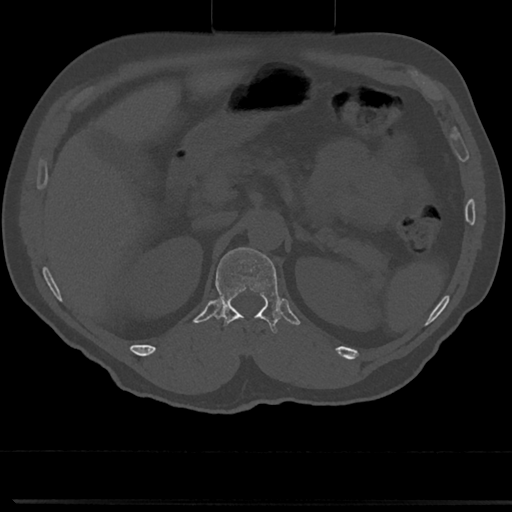
CT including the spine, one axial slice. Position 145 of 817 along the scan axis. 120 kVp. Bone window (W 1800 / L 400 HU). 0.5 mm slice thickness. 512 × 512 image matrix, field of view 355 × 355 mm. Male patient, age 61 years. From the clinical record (not read from this slice): primary cancer: prostate.
Outlined on this slice (semi-automatic segmentation, software-assisted and operator-edited):
- T12 vertebra: bounding box [x1, y1, x2, y2] px = [212, 246, 280, 340]